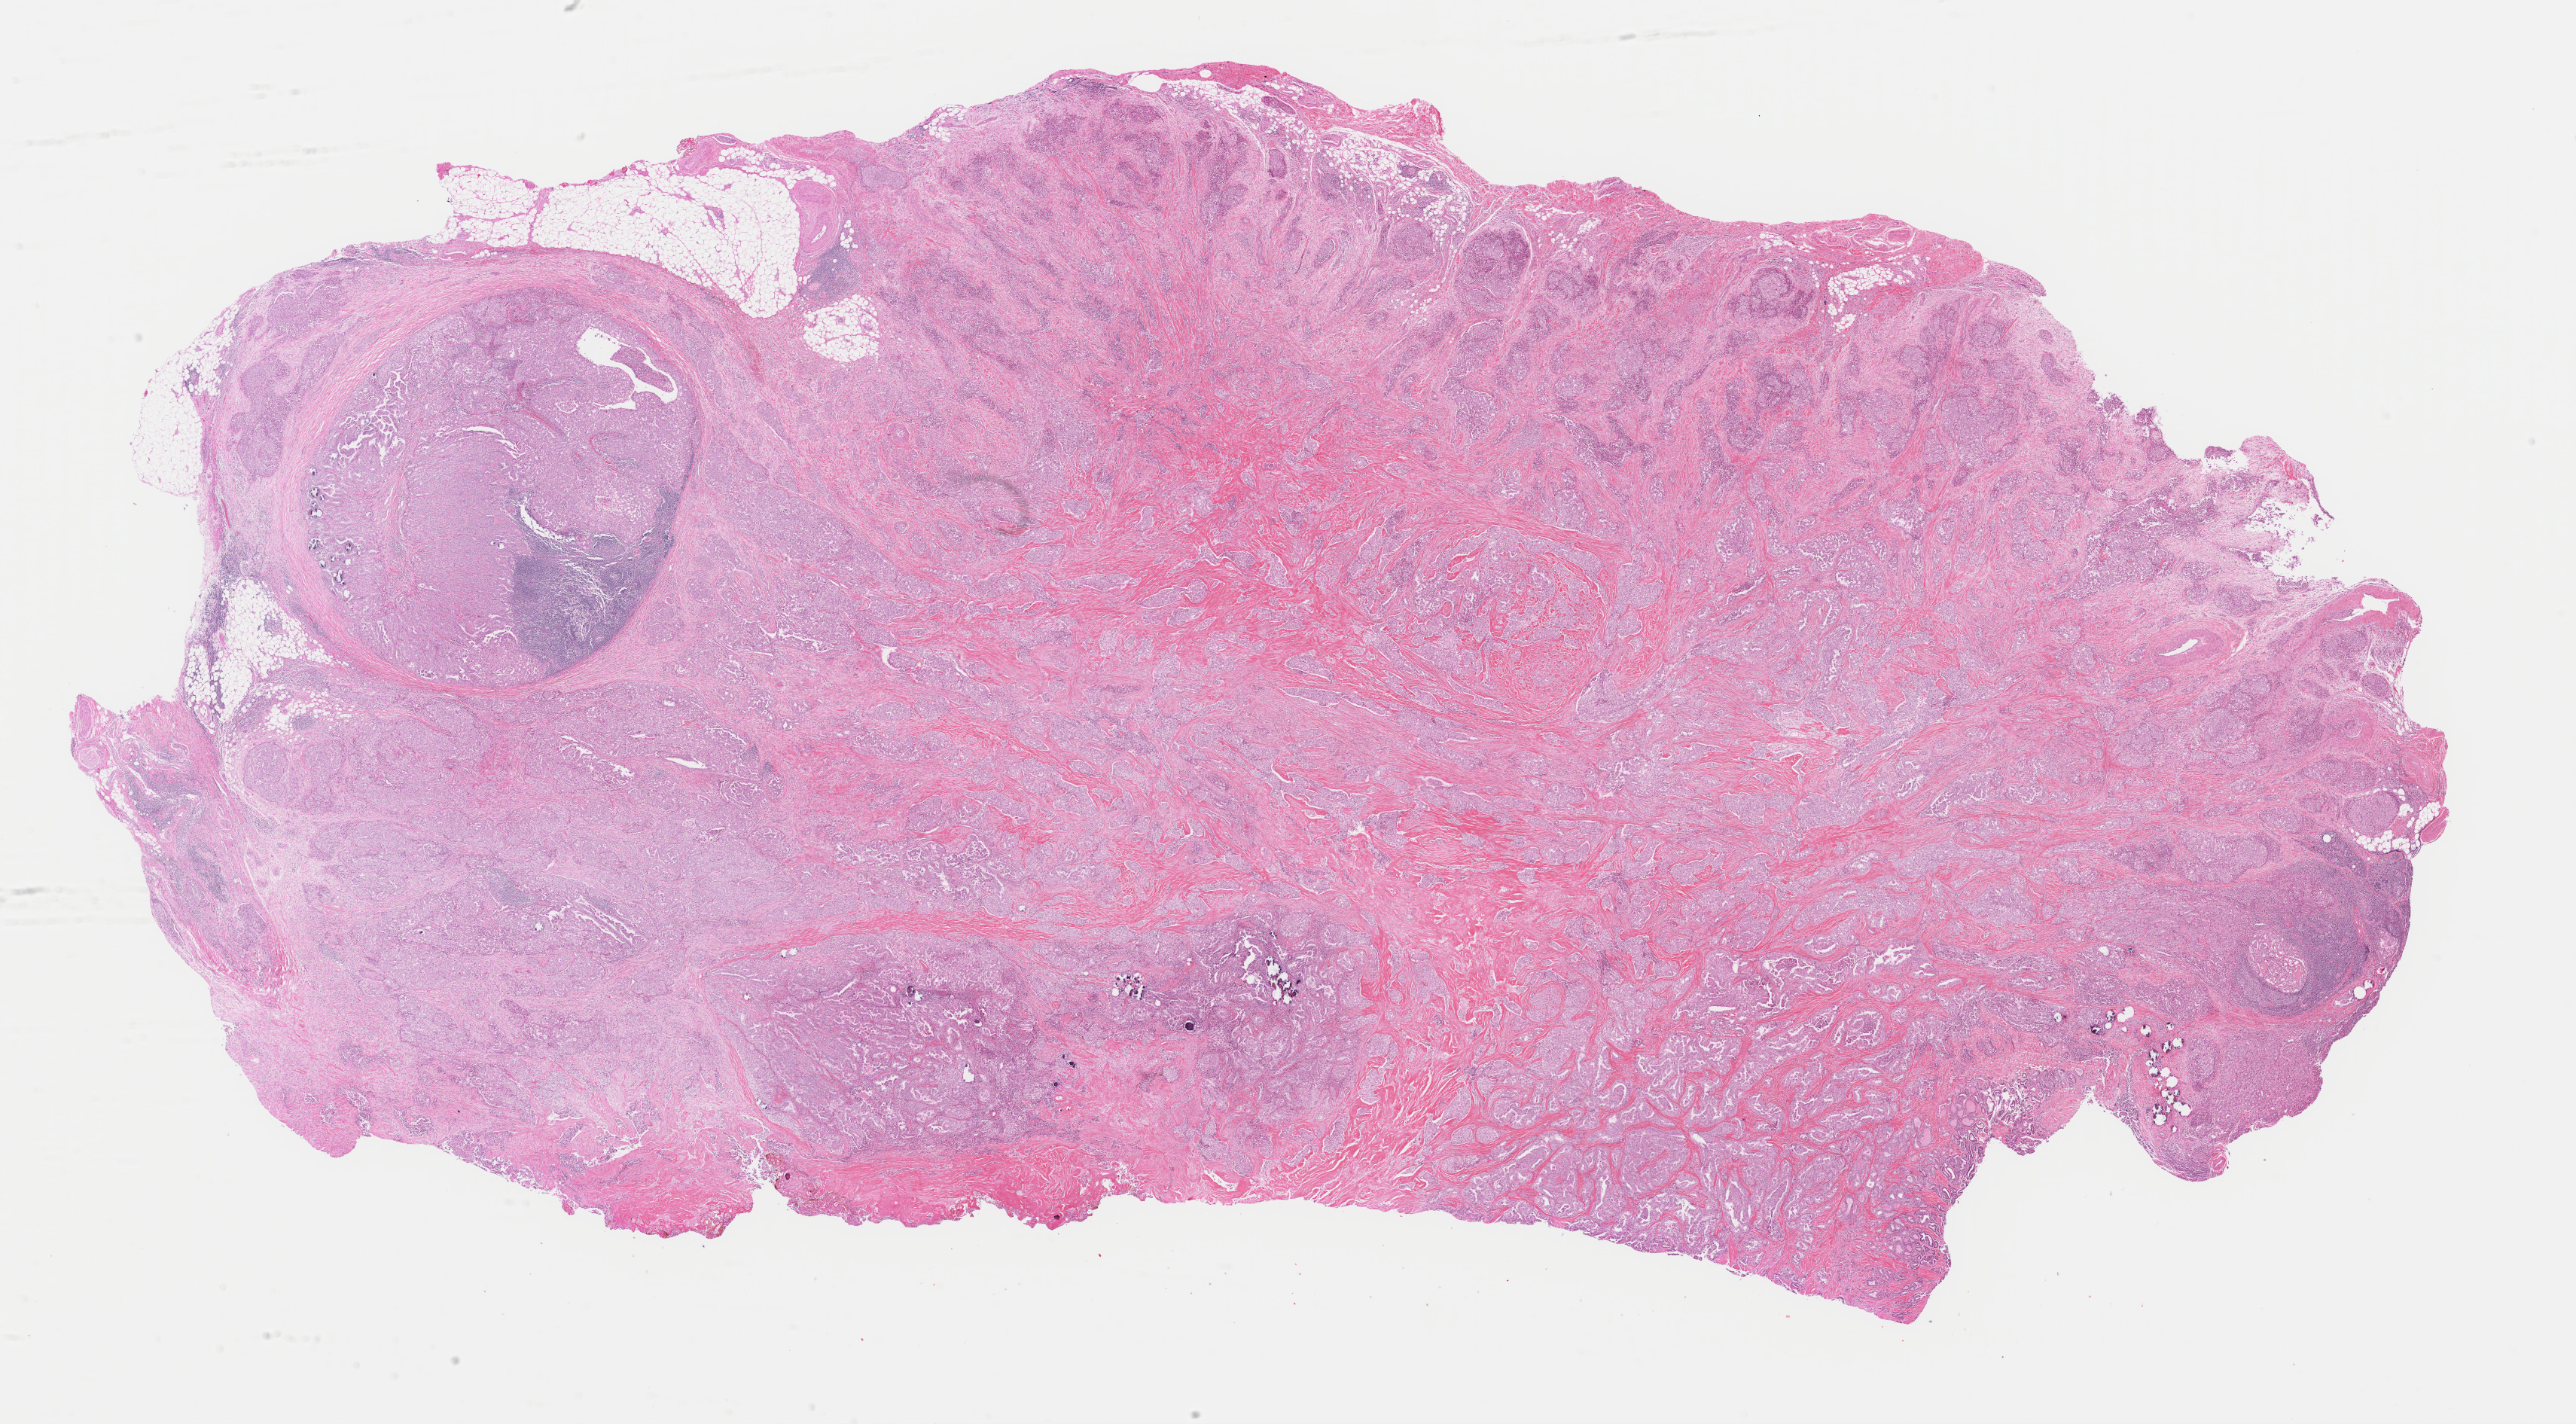
H&E whole-slide image — low-resolution overview of the scanned area, about 27.0 x 14.9 mm. FFPE section. Sample: primary tumour, thyroid. Female, age 69 years at initial diagnosis.
* pathologic diagnosis: Papillary adenocarcinoma, NOS (thyroid gland)
* AJCC pathologic stage: IV (6th edition)